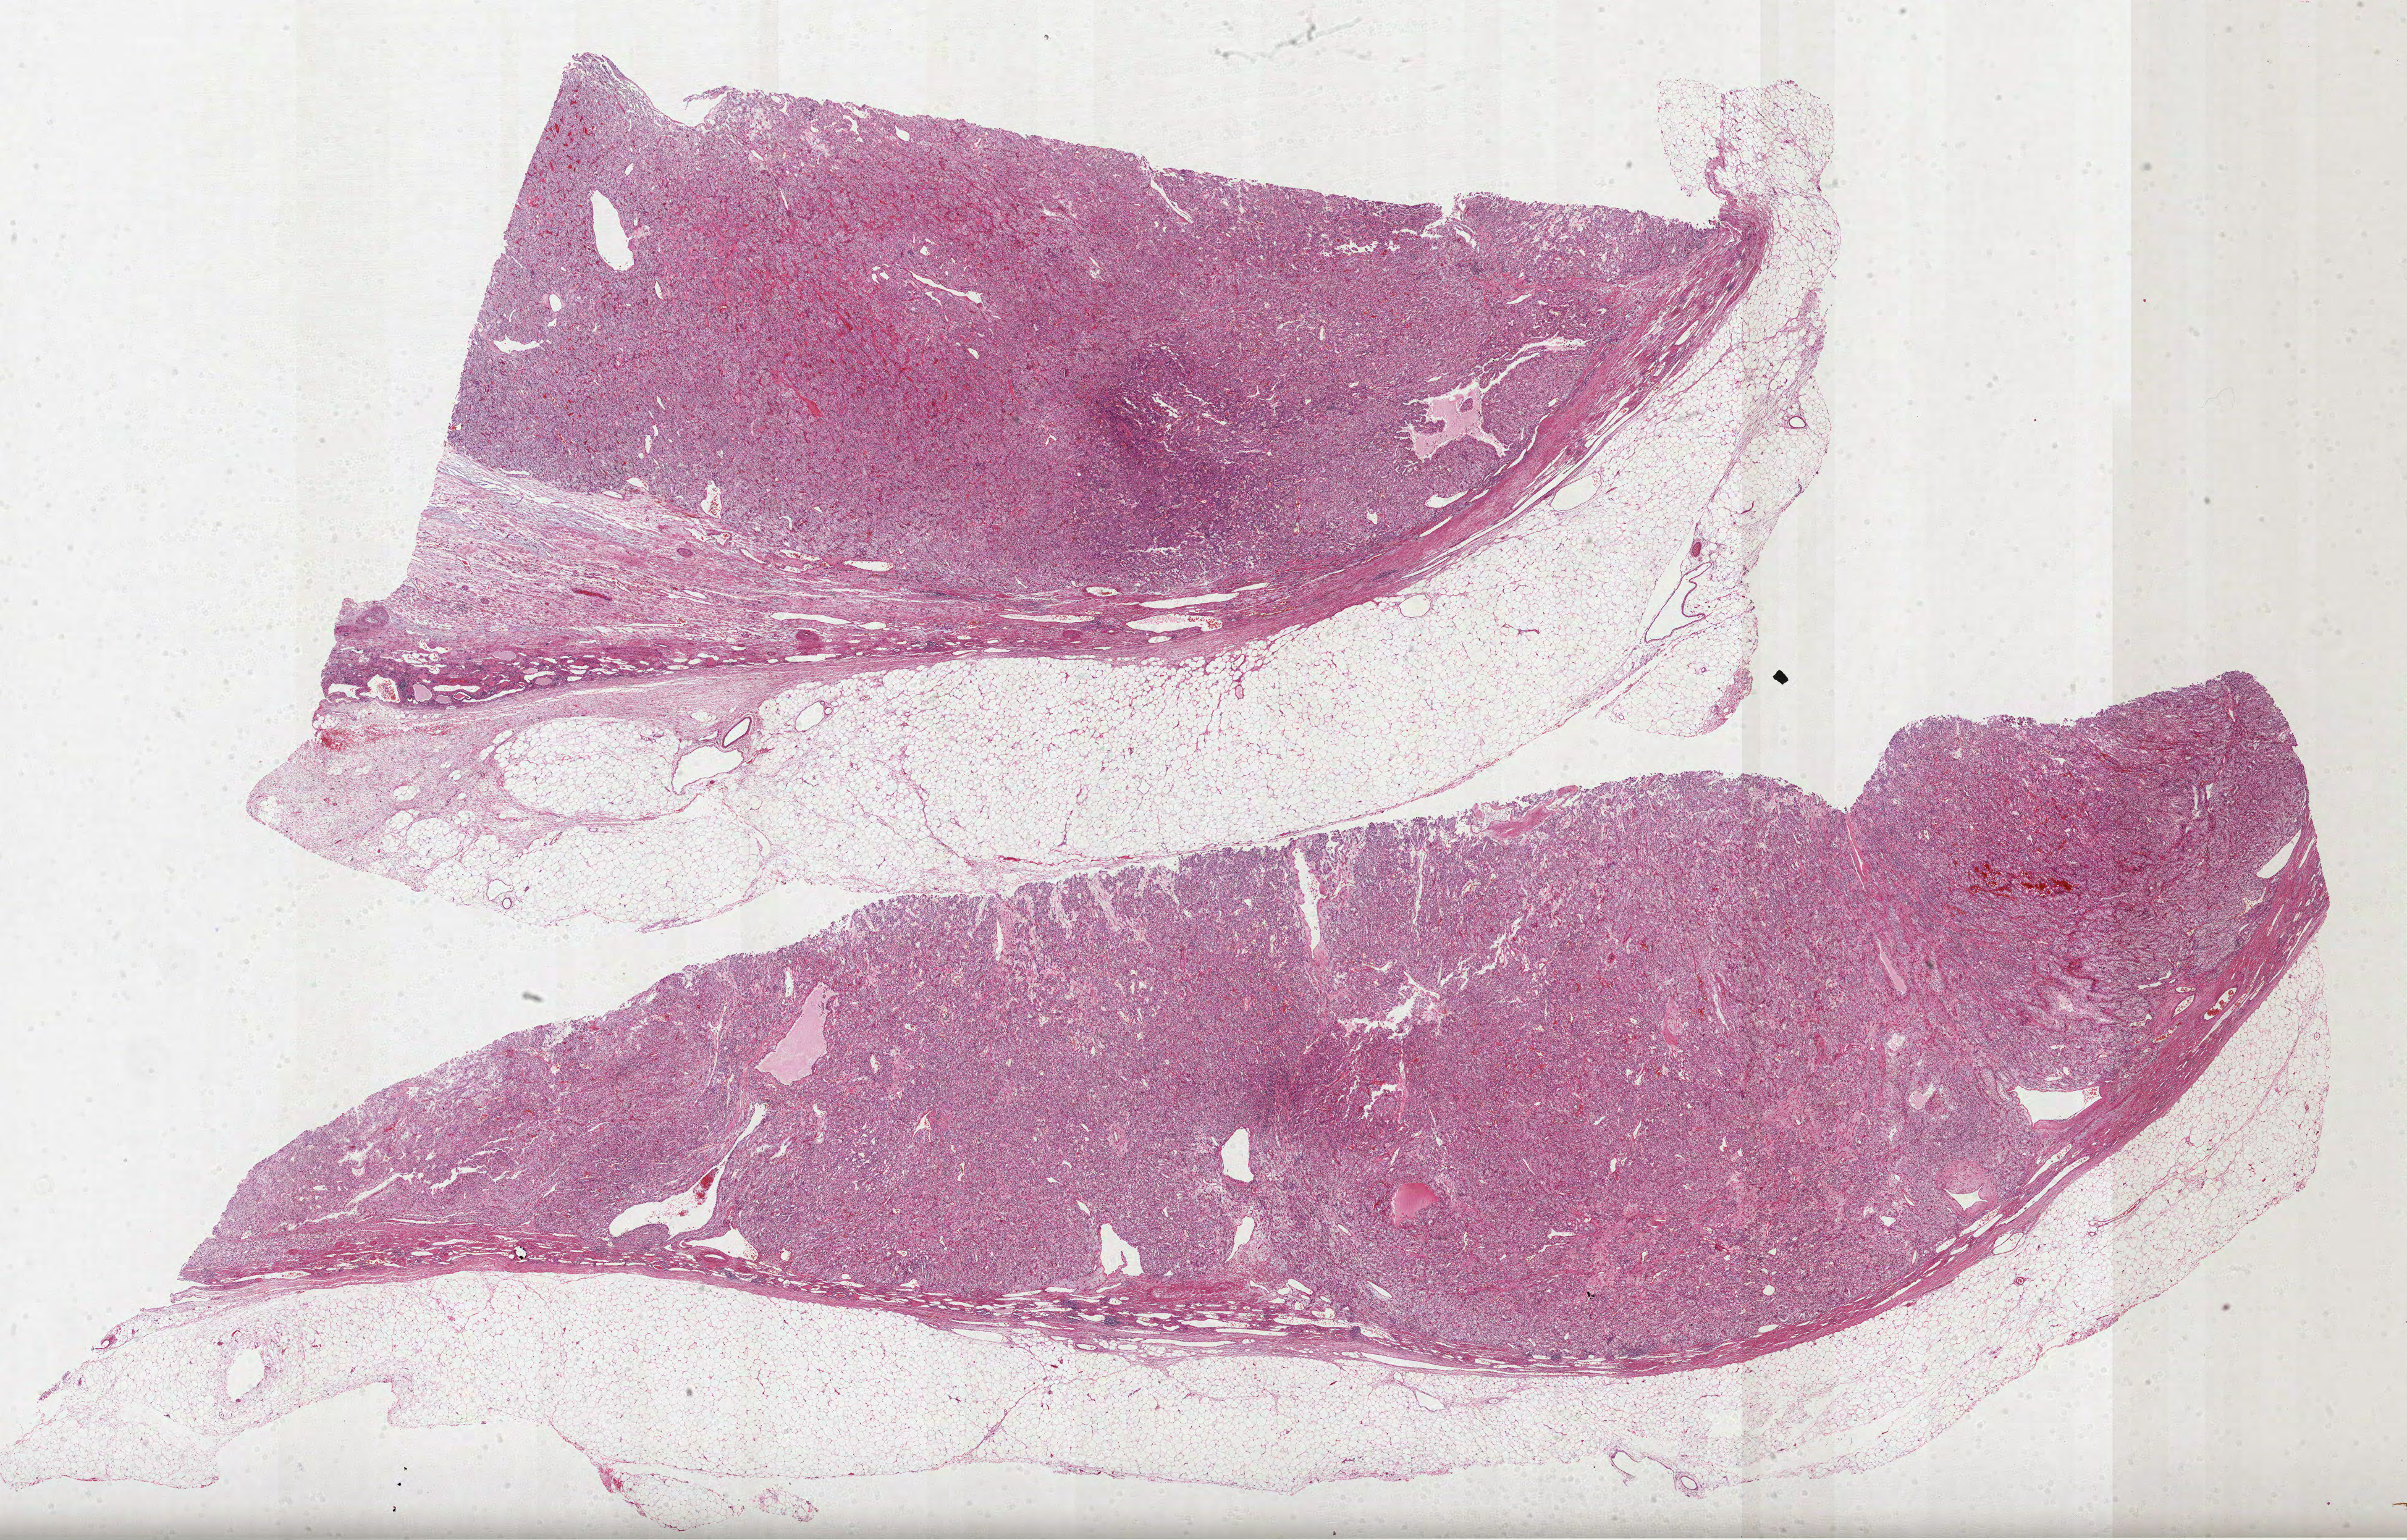
Whole-slide histology image, H&E-stained — whole scanned area (about 31.4 x 20.1 mm, from a 40x scan) shown as a low-resolution overview, FFPE section, kidney, primary tumour sample. Female, age 80 years at initial diagnosis. Histologic grade: G2 (moderately differentiated).
TNM: T1b N0 M0. Diagnosis: Clear cell adenocarcinoma, NOS. AJCC pathologic stage: I.